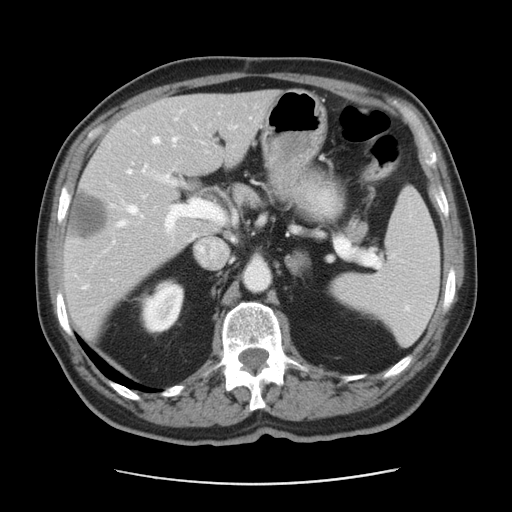
Contrast-enhanced abdominal CT, one axial slice; slice 26 of 42 in the series (ordered by position); 120 kVp; intravenous contrast given; soft-tissue window (W 400 / L 40 HU); 512 × 512 image matrix, field of view 370 × 370 mm. Male patient, age 73 years. From the clinical record (not read from this slice): diagnosis: colorectal cancer liver metastases, imaged before liver resection; multiple liver metastases: yes; largest metastasis: 0.5 cm; disease in both lobes: no.
Structures marked on this image (outlined manually by an expert reader):
- hepatic veins: bounding box [x1, y1, x2, y2] px = [82, 138, 176, 289]
- liver: [65, 93, 274, 336]
- planned liver remnant (the part of the liver to remain after resection): [110, 92, 274, 234]
- portal vein (with intrahepatic branches): [128, 169, 212, 229]
- liver metastasis: [71, 193, 108, 238]